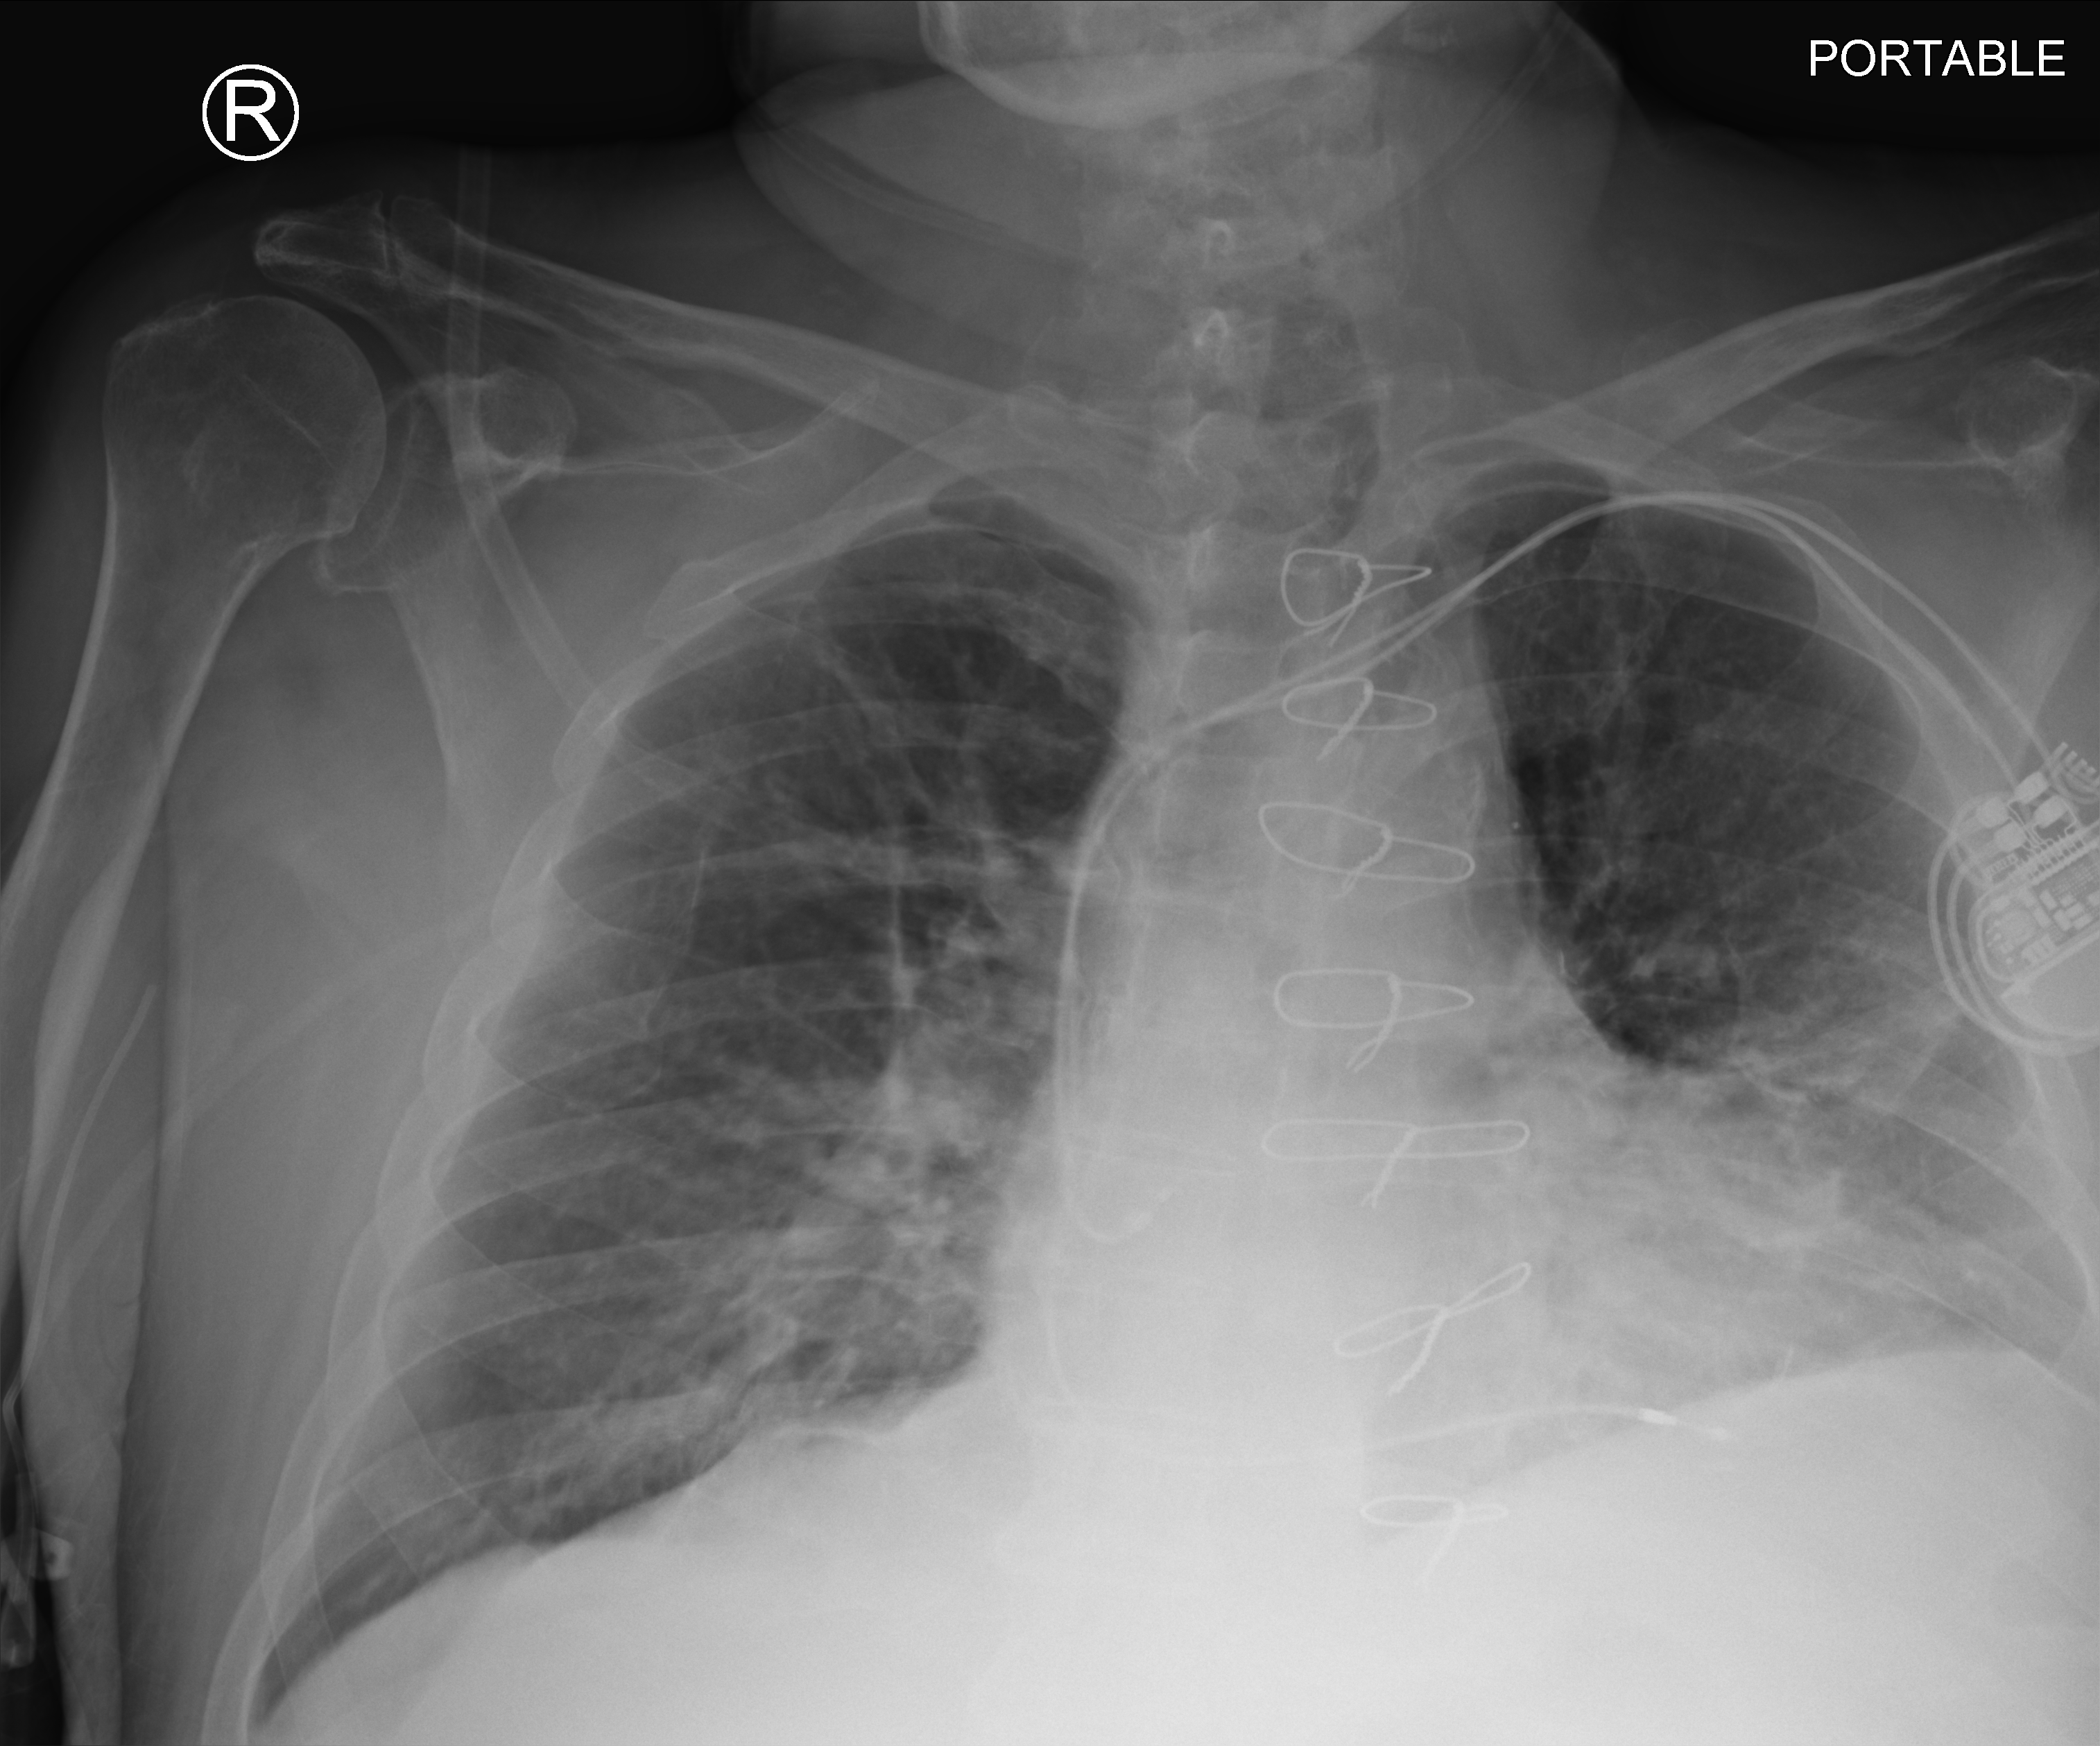
Chest X-ray (portable); anteroposterior (AP) projection. Patient hospitalised with COVID-19; male, aged 75–90 years.
Hospital-stay facts (about this admission, not read from this image; timing relative to this image not recorded): length of hospital stay: 6 days.